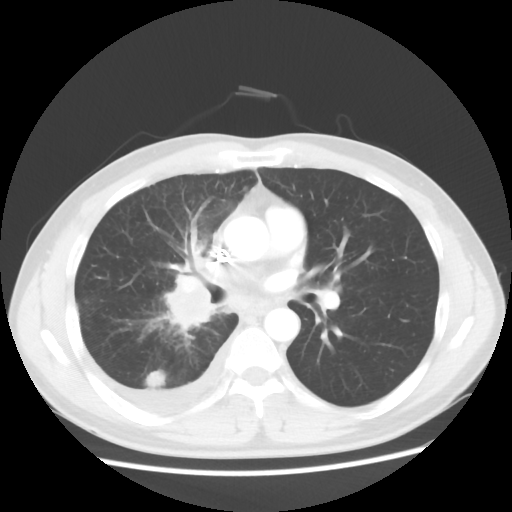
Chest CT, one axial slice. Reconstruction kernel STANDARD. Lung window (W 1500 / L -600 HU). 512 × 512 image matrix, field of view 360 × 360 mm. Patient: male, 46 years. Case-level facts recorded for this patient, not image findings: clinical TNM (as recorded): T2 N3 M1.
Annotated regions visible in this slice (rectangle marked by the reading radiologist):
- lung tumour (recorded histology: adenocarcinoma): bounding box <160,267,222,340> (left, top, right, bottom; pixels)